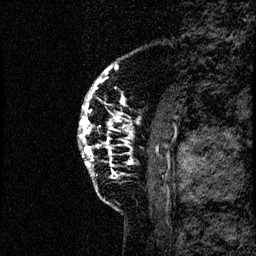
Breast MRI (dynamic contrast-enhanced), one sagittal slice; dynamic contrast-enhanced study with each time point stored as its own series, time point 2 of 4 at this slice position (early post-contrast, ordered by acquisition time); 1.5 T; TE 4.2 ms, TR 17.6 ms; 2 mm slice thickness; 256 × 256 image matrix, field of view 200 × 200 mm. Patient: female, 40 years. From the clinical record (not read from this slice): setting: breast cancer imaged before/during neoadjuvant chemotherapy; receptor status: HER2-positive.
Annotated regions visible in this slice (semi-automatic segmentation, software-assisted and operator-edited):
- analysis volume of interest (the breast-tissue region the enhancement analysis was run in; not a lesion): bounding box <74,55,185,206> (left, top, right, bottom; pixels)
- tumour enhancement mask (voxels above the 100 % enhancement threshold inside the analysis volume of interest): <78,65,129,178>